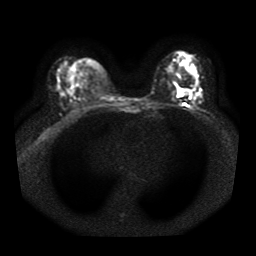
Breast MRI, one axial slice. Slice 24 of 41 in the series (ordered by position). Diffusion-weighted series; image 2 of 4 stored at this slice position (different b-values; order by instance number). 1.5 T. 5 mm slice thickness. 256 × 256 image matrix, field of view 330 × 330 mm. Female patient.
Annotated regions visible in this slice (outlined manually by an expert reader):
- tumour on diffusion-weighted imaging: bounding box [x1, y1, x2, y2] px = [180, 89, 191, 96]